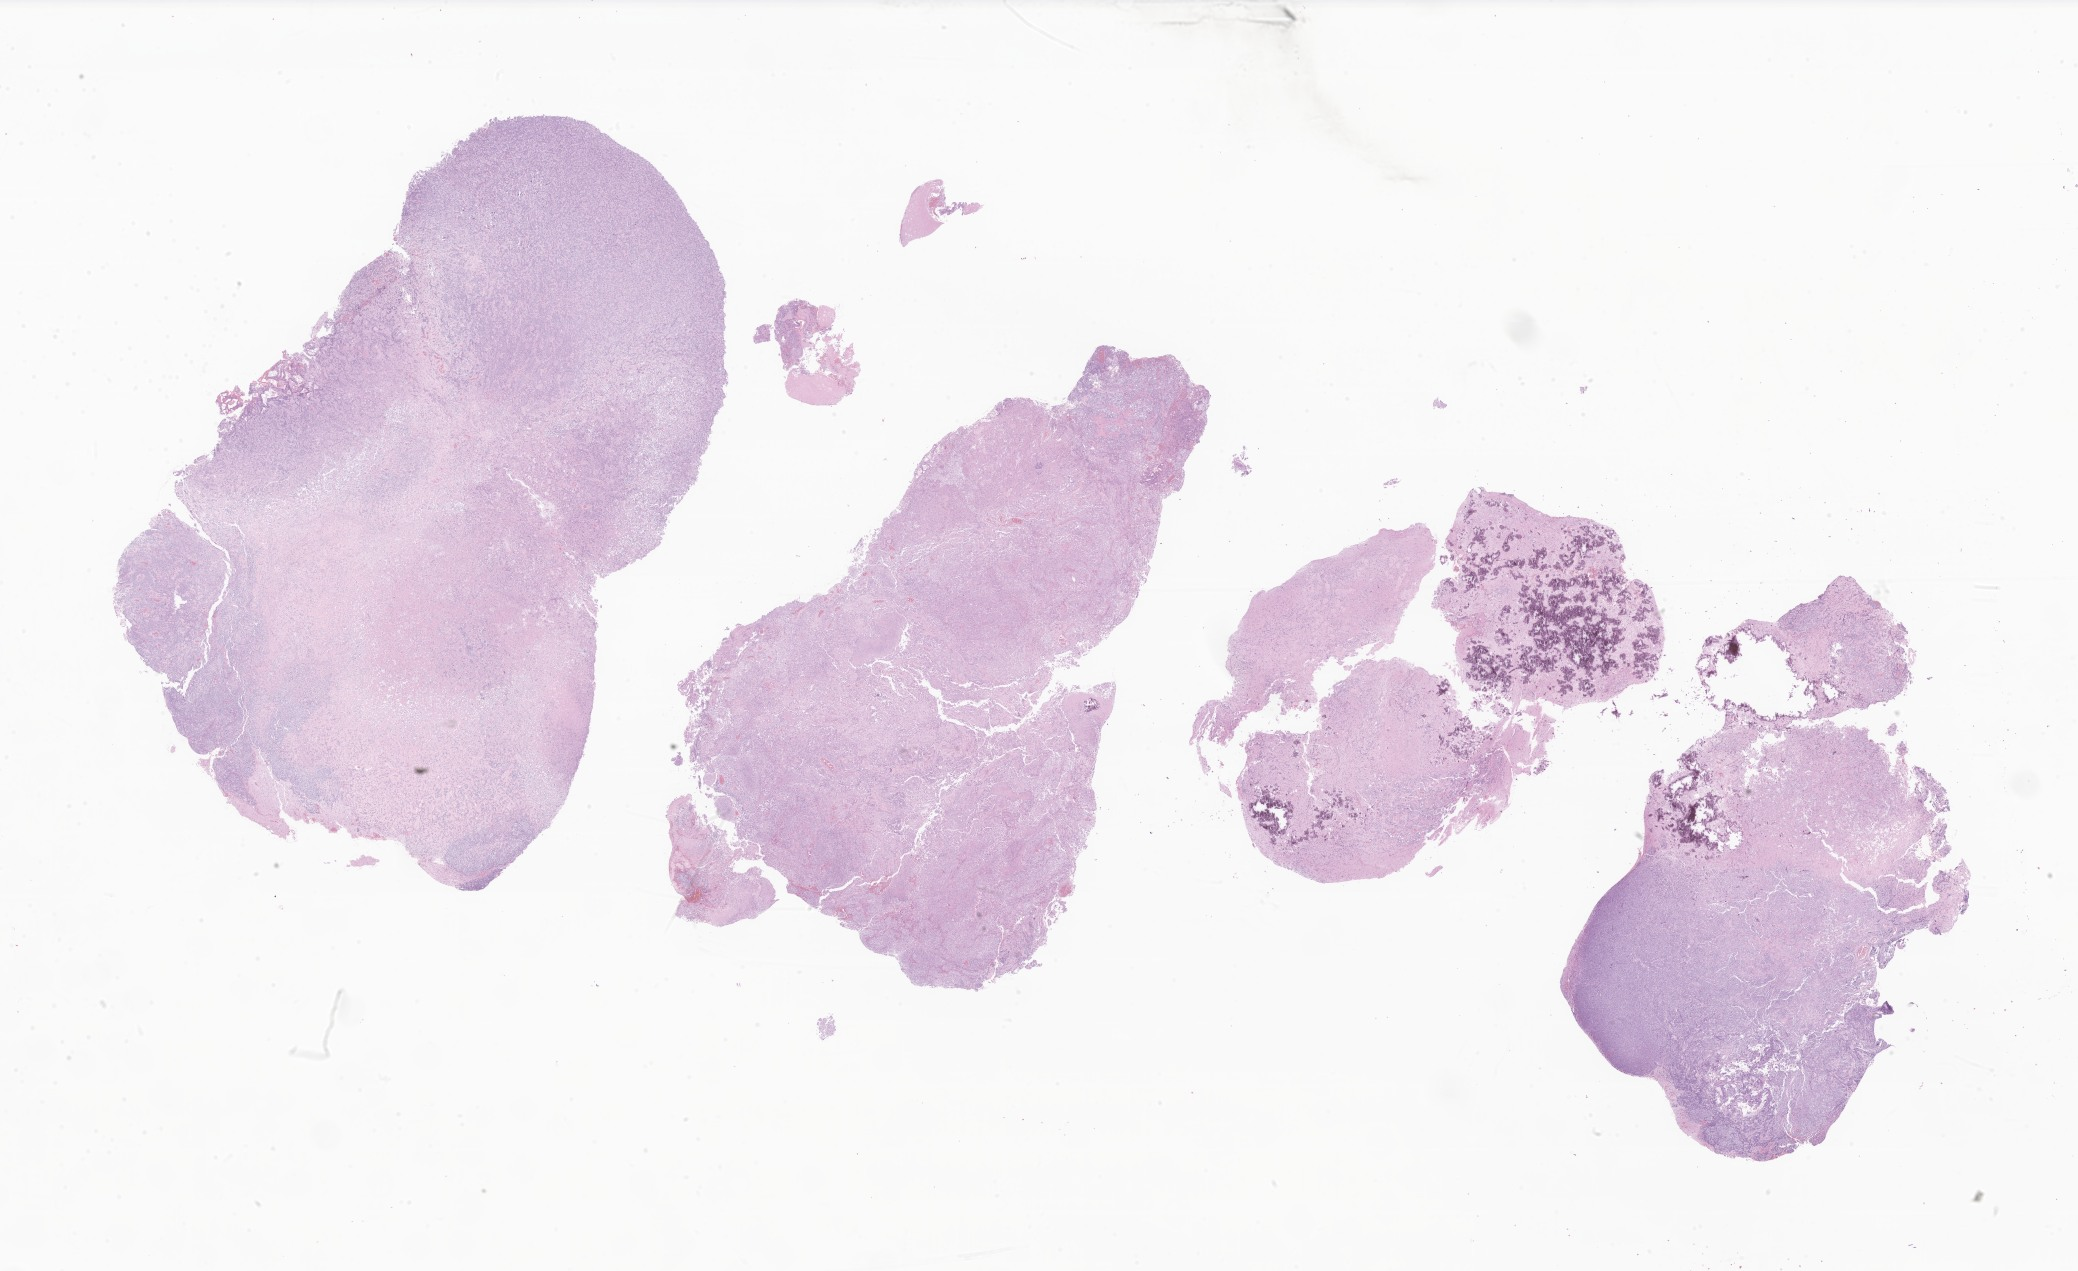
H&E whole-slide image of tumor tissue from the temporal lobe — shown as a low-resolution overview of the whole scanned area (about 35.1 x 21.4 mm); FFPE section. Patient: male, age 155 months (12 years 11 months).
• recorded diagnosis: Ependymoma, NOS